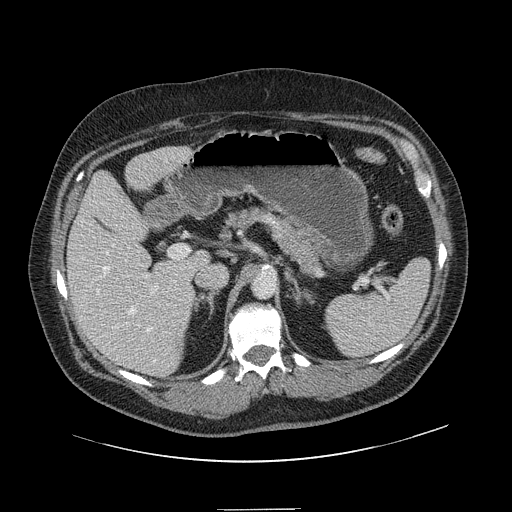
Contrast-enhanced abdominal CT, one axial slice; slice 84 of 154 in the series (ordered by position); 120 kVp; intravenous contrast given; soft-tissue window (W 400 / L 40 HU); 2.5 mm slice thickness; 512 × 512 image matrix, field of view 451 × 451 mm. Male patient, age 61 years. From the clinical record (not read from this slice): diagnosis: colorectal cancer liver metastases, imaged before liver resection; multiple liver metastases: yes; largest metastasis: 2.6 cm; disease in both lobes: yes.
Structures marked on this image (expert manual segmentation):
- hepatic veins: bounding box (x1, y1, x2, y2) in pixels: (103, 244, 156, 362)
- liver: (68, 147, 208, 376)
- planned liver remnant (the part of the liver to remain after resection): (69, 149, 208, 366)
- portal vein (with intrahepatic branches): (96, 252, 158, 297)